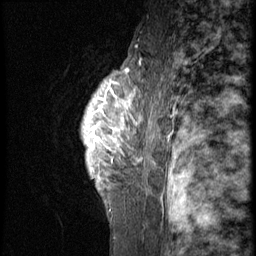
Breast MRI (dynamic contrast-enhanced), one sagittal slice. 3 images stored at this slice position (order not interpretable as contrast timing). 1.5 T. TE 4.2 ms, TR 9 ms. 2.5 mm slice thickness. 256 × 256 image matrix, field of view 180 × 180 mm. Female patient, age 50 years. From the clinical record (not read from this slice): setting: breast cancer imaged before/during neoadjuvant chemotherapy; receptor status: triple-negative.
Structures marked on this image (semi-automatically segmented with operator editing):
- analysis volume of interest (the breast-tissue region the enhancement analysis was run in; not a lesion): bounding box (x1, y1, x2, y2) in pixels: (67, 63, 127, 214)
- tumour enhancement mask (voxels above the 140 % enhancement threshold inside the analysis volume of interest): (83, 75, 126, 179)